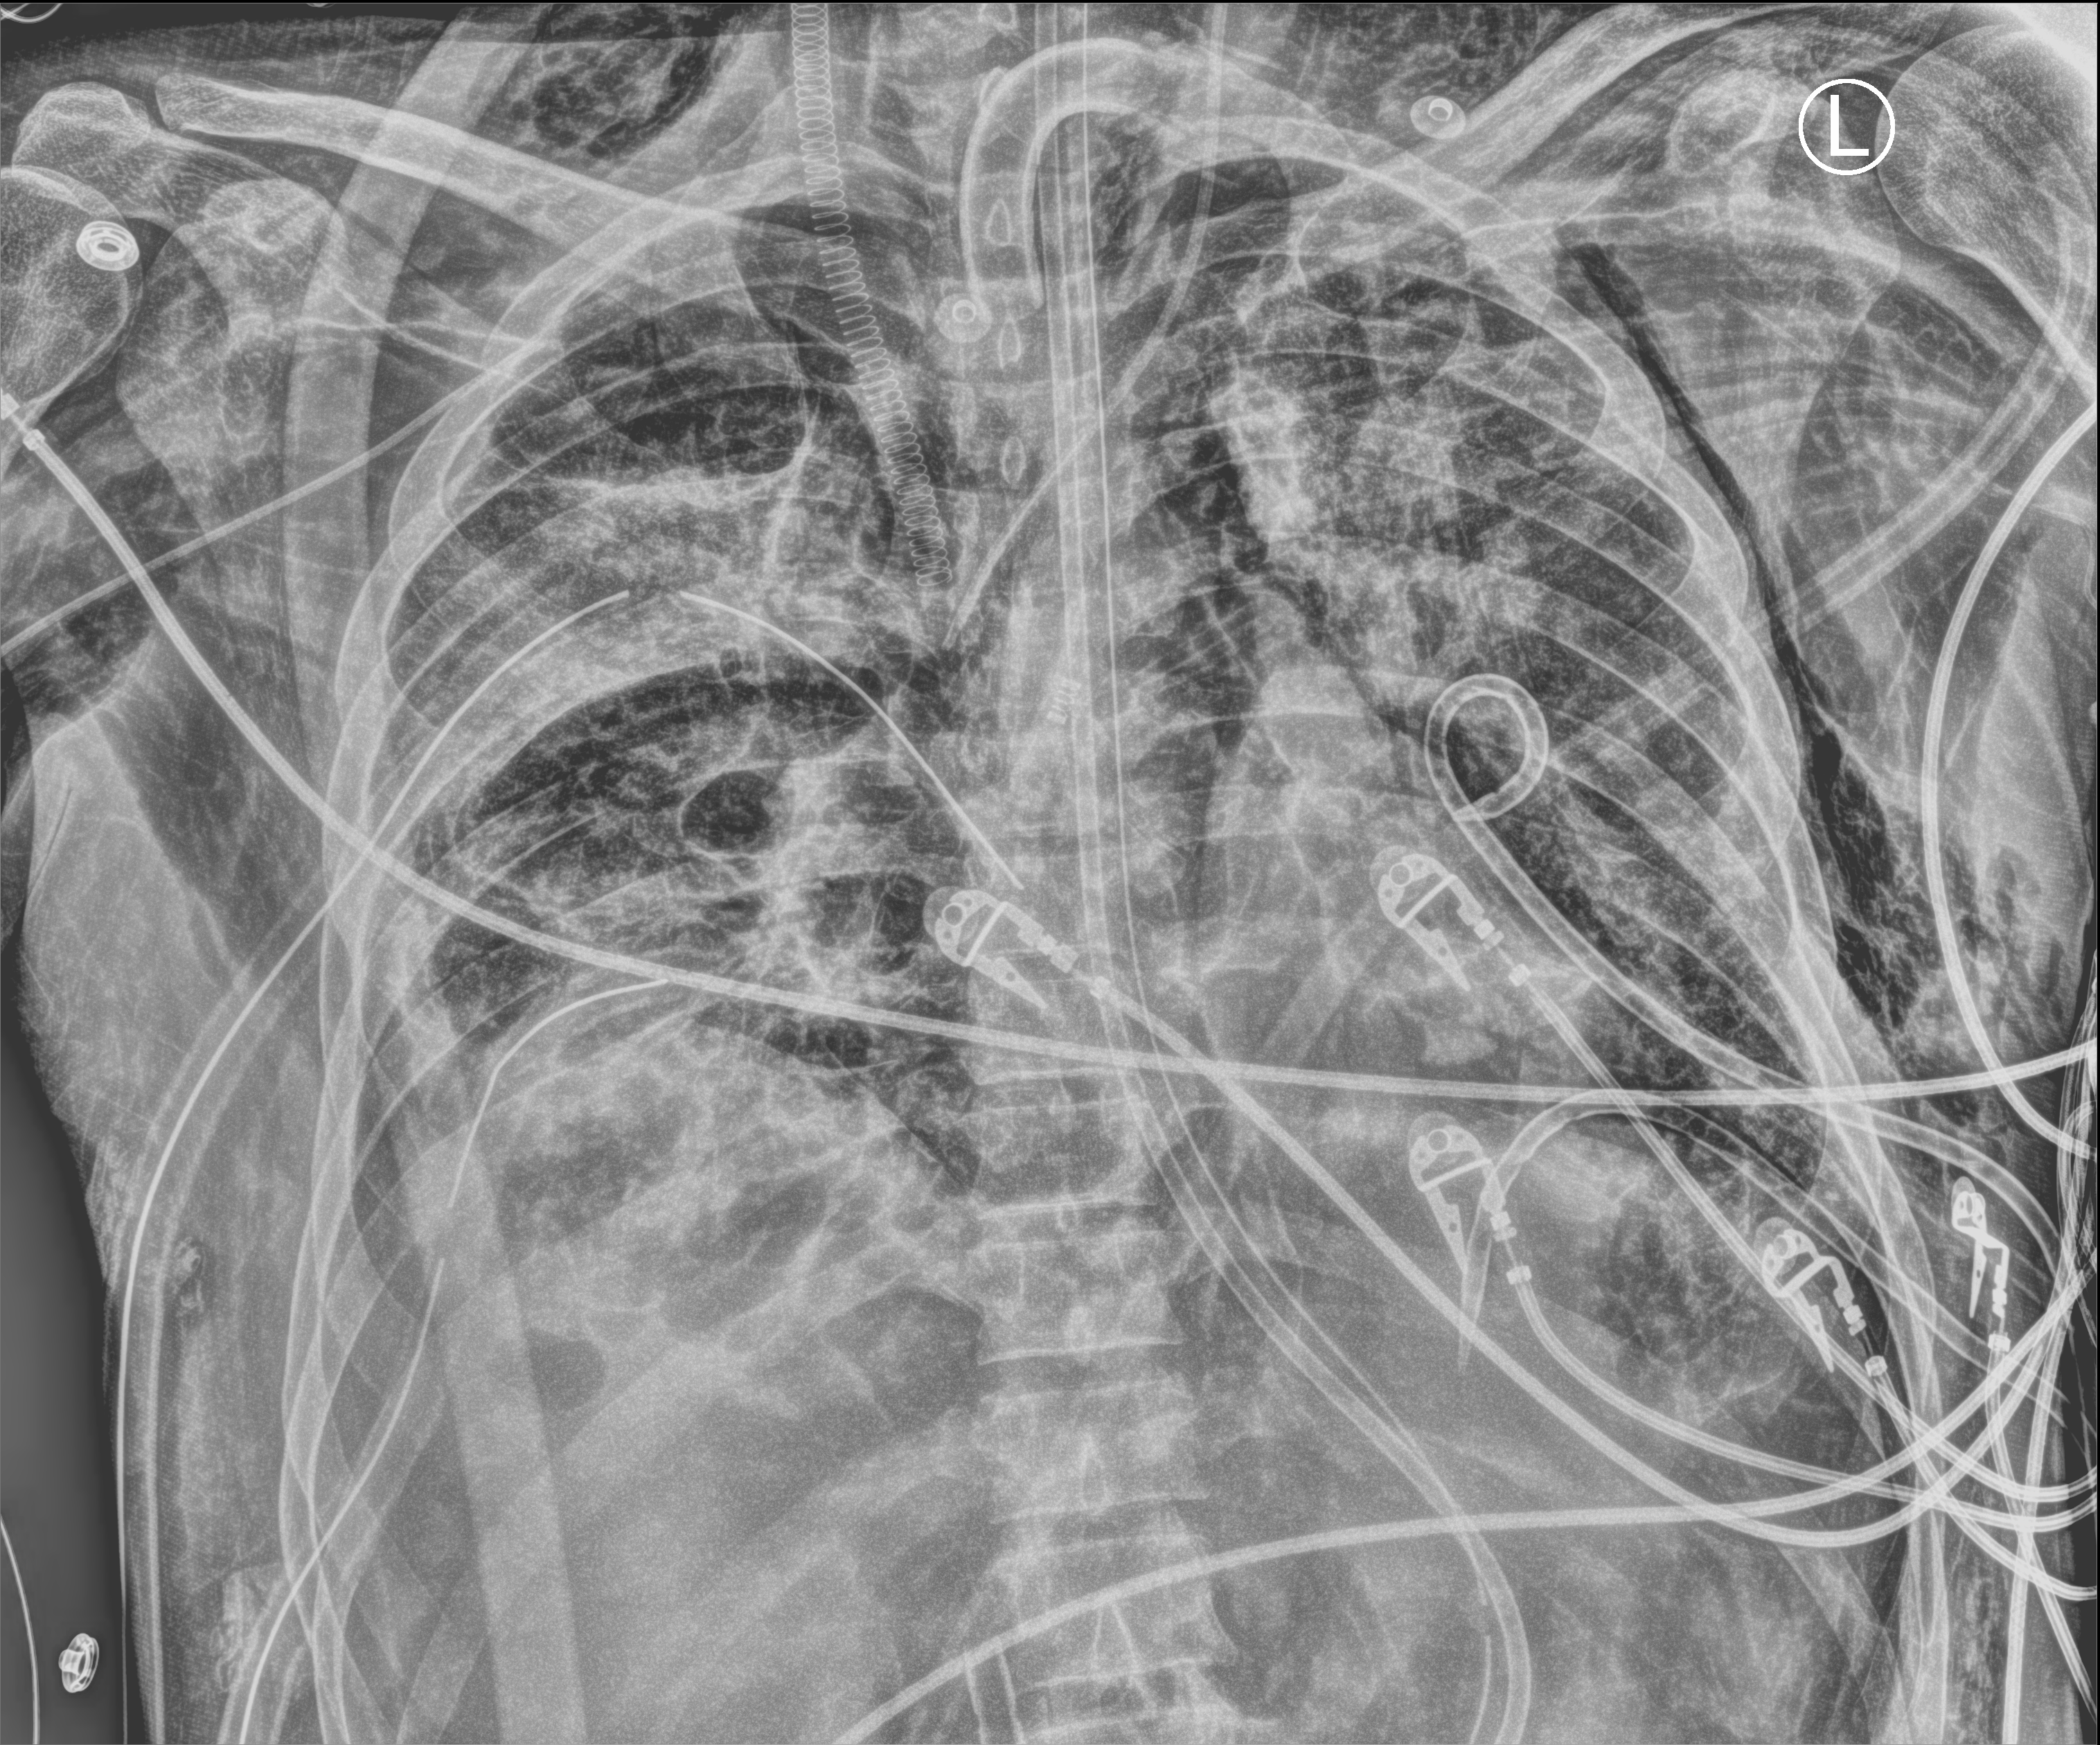
Portable chest radiograph; anteroposterior (AP) projection. Patient hospitalised with COVID-19, aged 18–59 years.
Hospital-stay facts (about this admission, not read from this image; timing relative to this image not recorded):
- COPD (admission record): no
- hypertension (admission record): no
- other chronic lung disease (admission record): no